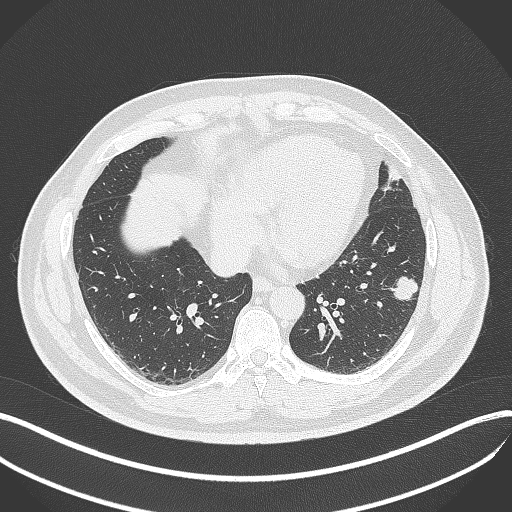
Chest CT, one axial slice; position 149 of 429 along the scan axis; reconstruction kernel B70f; 120 kVp; lung window (W 1500 / L -600 HU); 512 × 512 image matrix. Patient: male, 39 years. From the clinical record (not read from this slice): clinical TNM (as recorded): T2a N0 M0; histopathological grade: G2-3.
Annotated regions visible in this slice (bounding box drawn by a radiologist):
- lung tumour (recorded histology: adenocarcinoma): box from (x=388, y=273) to (x=421, y=302) px